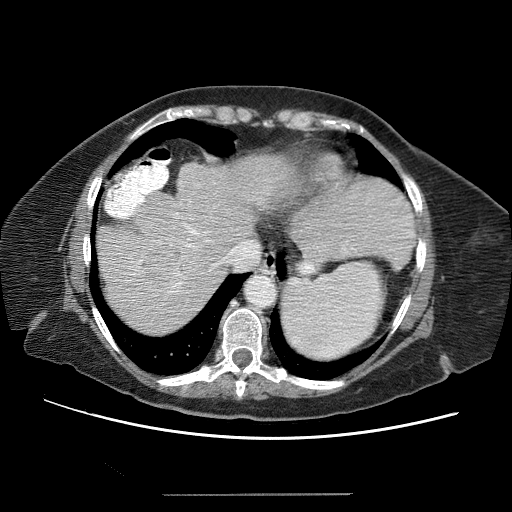
Contrast-enhanced abdominal CT (liver protocol), one axial slice. Slice 51 of 65 in the series (ordered by position). Reconstruction kernel STANDARD. 120 kVp. Soft-tissue window (W 400 / L 40 HU). 512 × 512 image matrix, field of view 380 × 380 mm. Case-level facts recorded for this patient, not image findings: diagnosis: hepatocellular carcinoma (patient treated with transarterial chemoembolisation; whether this scan precedes or follows treatment is not stated here); TNM stage (as recorded): Stage-IIIB; Child-Pugh class: A; tumour differentiation: moderately differentiated.
Structures marked on this image (semi-automatic segmentation, software-assisted and operator-edited):
- liver parenchyma outside the tumour (the mass and vessels are separate outlines, so this box may not span the whole liver): bounding box [x1, y1, x2, y2] px = [98, 158, 282, 326]
- mass: [125, 232, 183, 295]
- liver vessels: [121, 176, 260, 298]